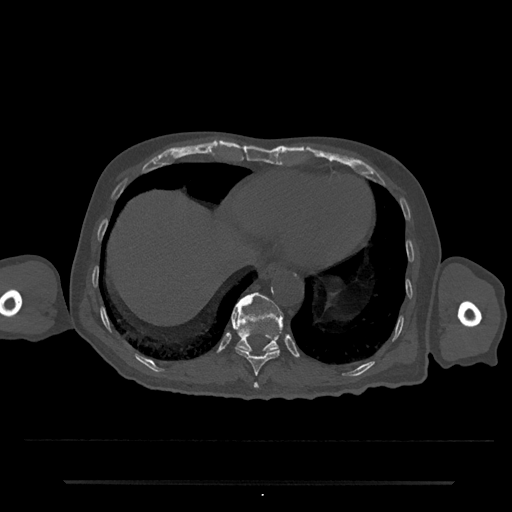
CT including the spine, one axial slice. Slice 291 of 797 in the series (ordered by position). Reconstruction kernel Br40s/3. 120 kVp. Bone window (W 1800 / L 400 HU). 0.5 mm slice thickness. 512 × 512 image matrix, field of view 427 × 427 mm. Patient: male, 74 years. Case-level facts recorded for this patient, not image findings: primary cancer: prostate.
Annotated regions visible in this slice (semi-automatically segmented with operator editing):
- T10 vertebra: bounding box [x1, y1, x2, y2] px = [231, 315, 282, 376]
- T11 vertebra: [232, 292, 283, 353]
- T9 vertebra: [253, 382, 259, 389]